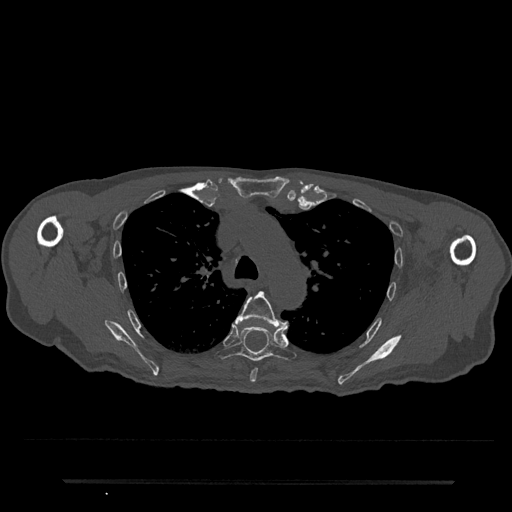
CT including the spine, one axial slice; slice 549 of 797 in the series (ordered by position); bone window (W 1800 / L 400 HU); 512 × 512 image matrix, field of view 427 × 427 mm. Male patient, age 74 years. Case-level facts recorded for this patient, not image findings: primary cancer: prostate.
Annotated regions visible in this slice (semi-automatic segmentation, software-assisted and operator-edited):
- T5 vertebra: bounding box [x1, y1, x2, y2] px = [236, 291, 289, 383]
- T6 vertebra: [215, 322, 296, 362]